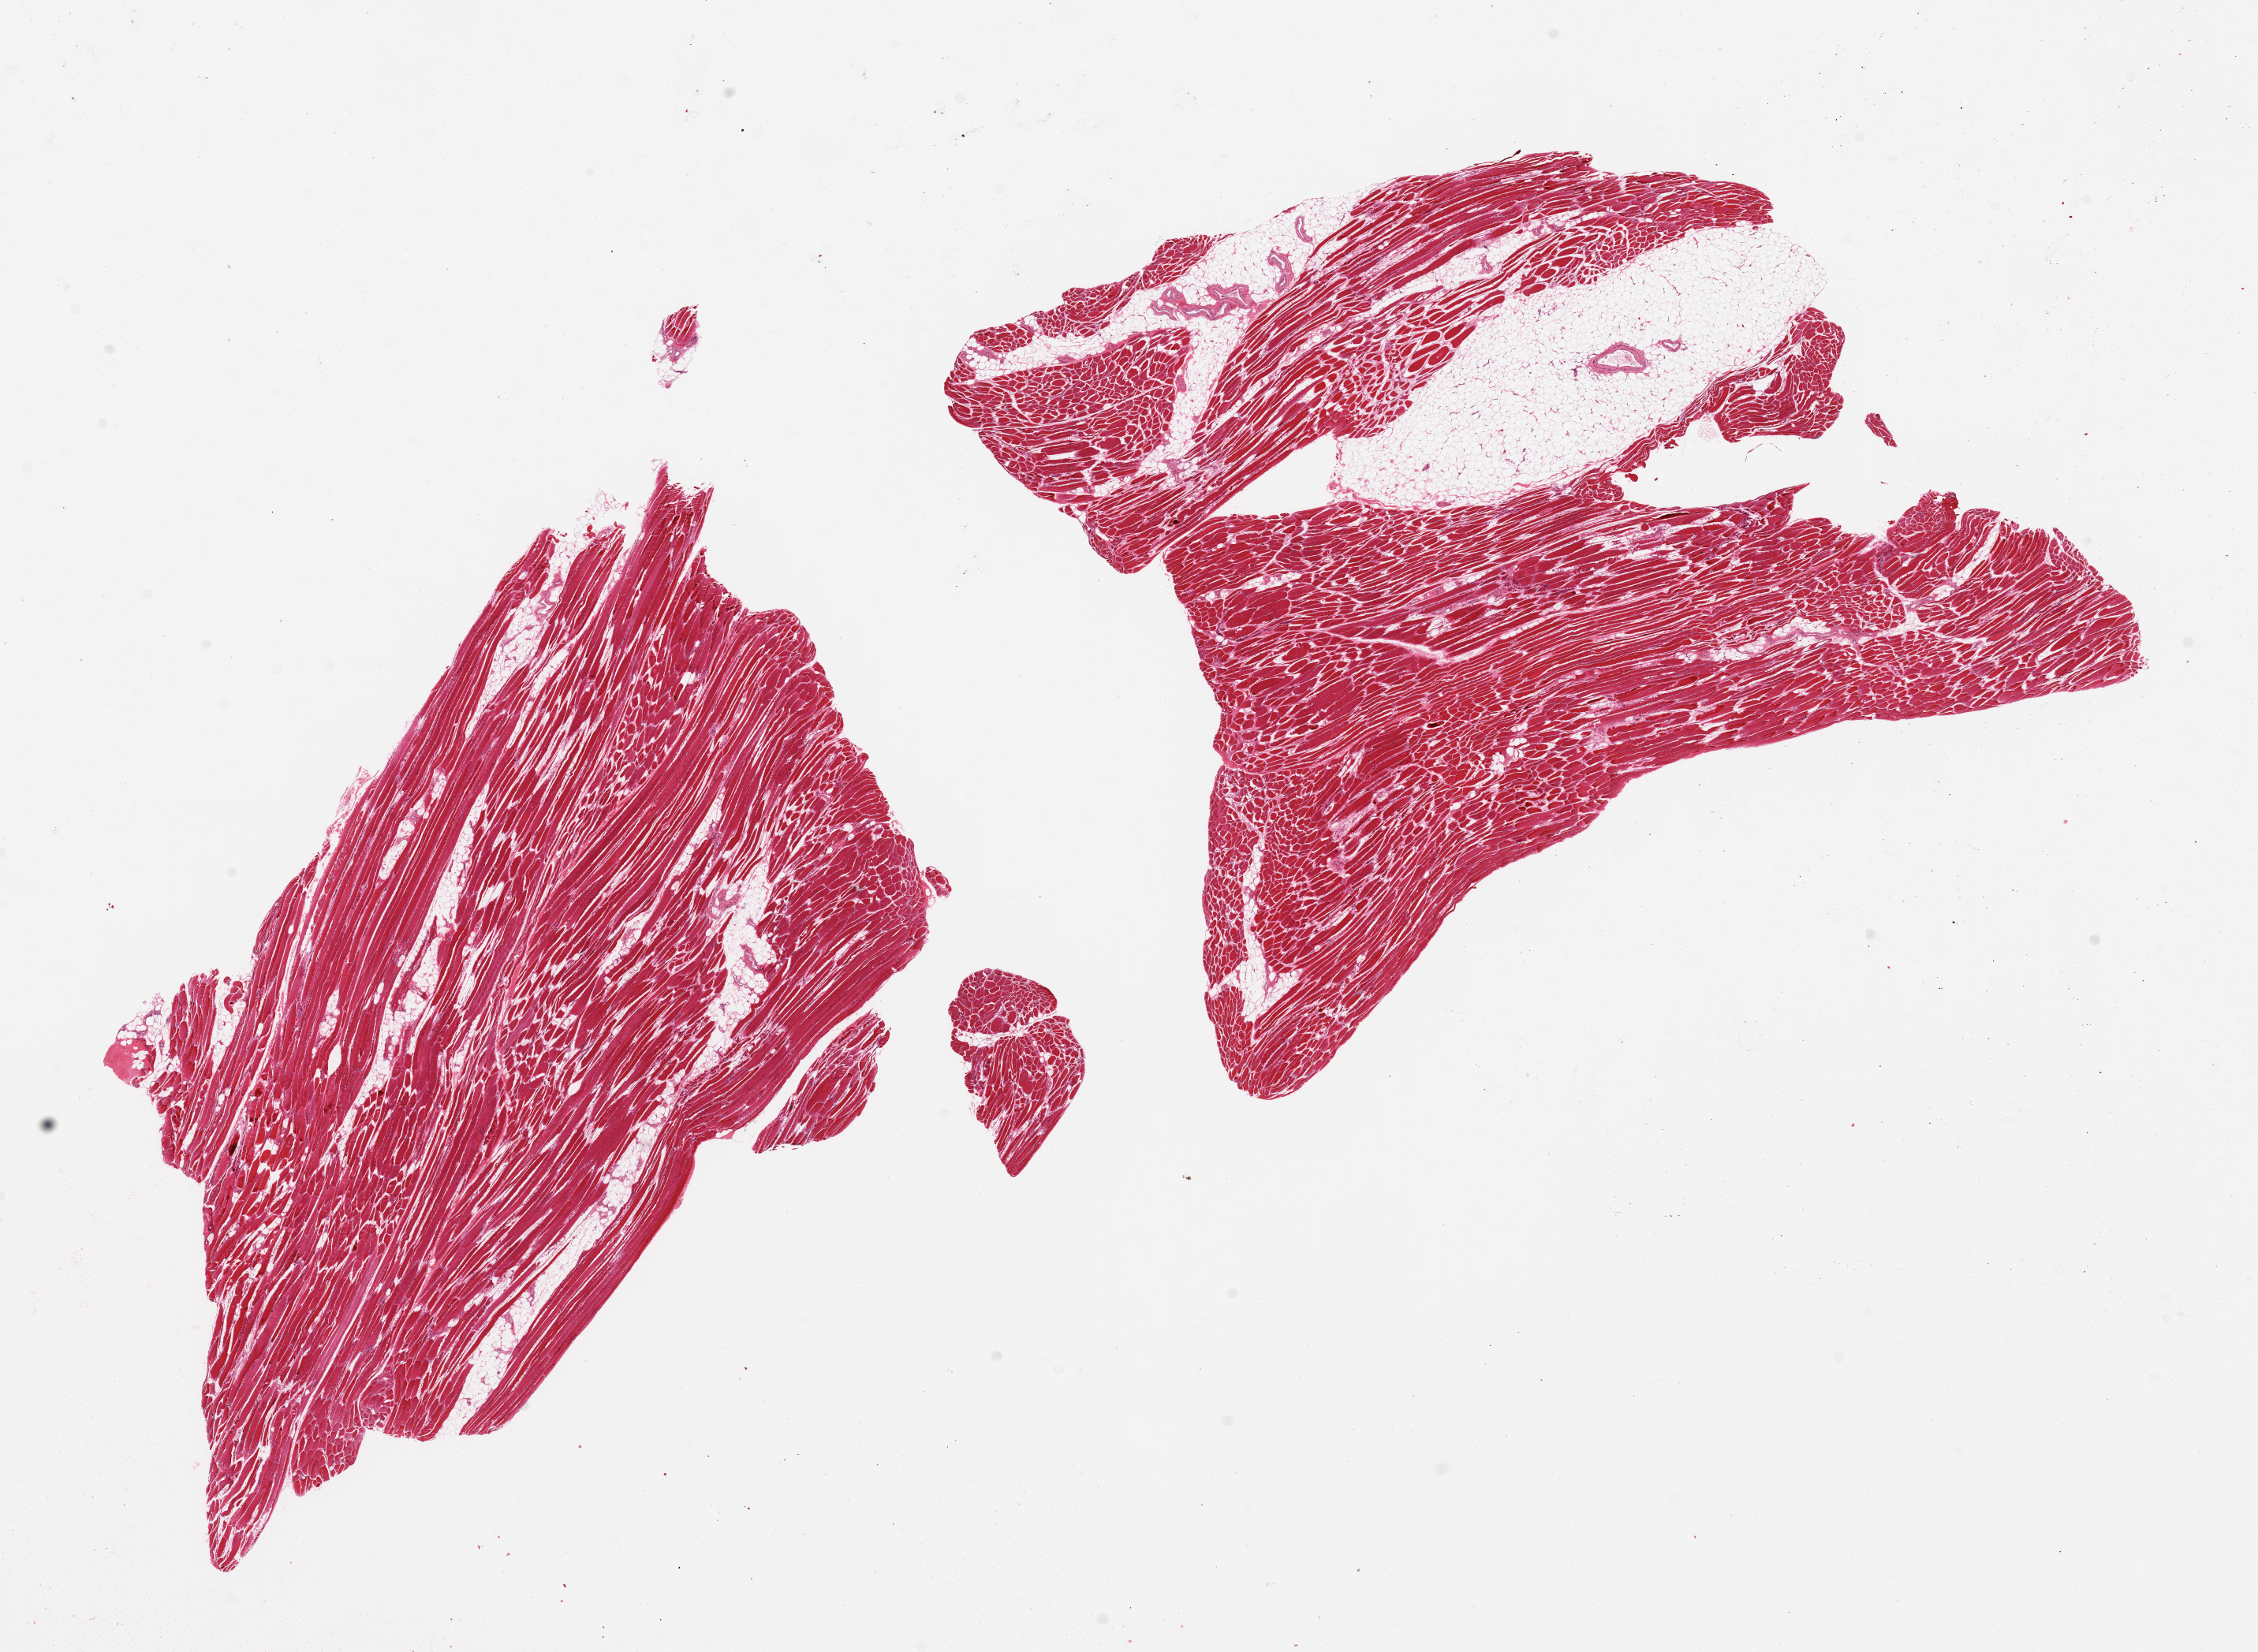
Haematoxylin and eosin whole-slide image — shown as a low-resolution overview of the whole scanned area (about 22.6 x 16.6 mm, acquisition: 20x scan), PAXgene-fixed paraffin-embedded (PFPE) section, sampled site (target tissue): skeletal muscle, tissue donor sample. Donor: male.
Pathologist's review note for this sample: 2 pieces; 1 has 20% fat.